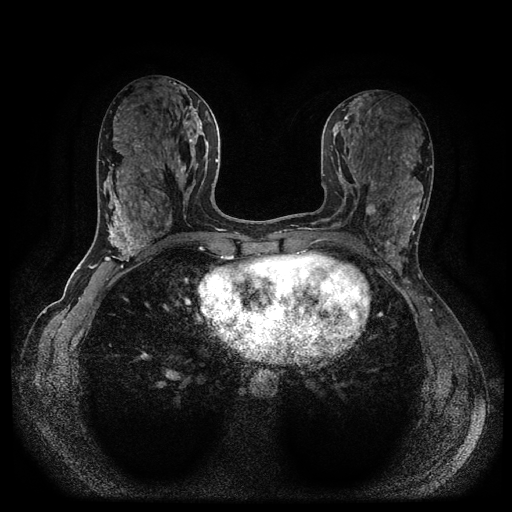
Breast MRI (dynamic contrast-enhanced, multi-phase), one axial slice; slice 46 of 116 in the series (ordered by position); dynamic contrast-enhanced series, time point 2 of 5 at this slice position (early post-contrast); 1.5 T; TE 2.6 ms, TR 5.4 ms; 2 mm slice thickness; 512 × 512 image matrix, field of view 340 × 340 mm. Female patient, age 43 years.
Structures marked on this image (semi-automatic segmentation, software-assisted and operator-edited):
- breast lesion (labelled benign in the annotation): bounding box (x1, y1, x2, y2) in pixels: (365, 200, 379, 217)